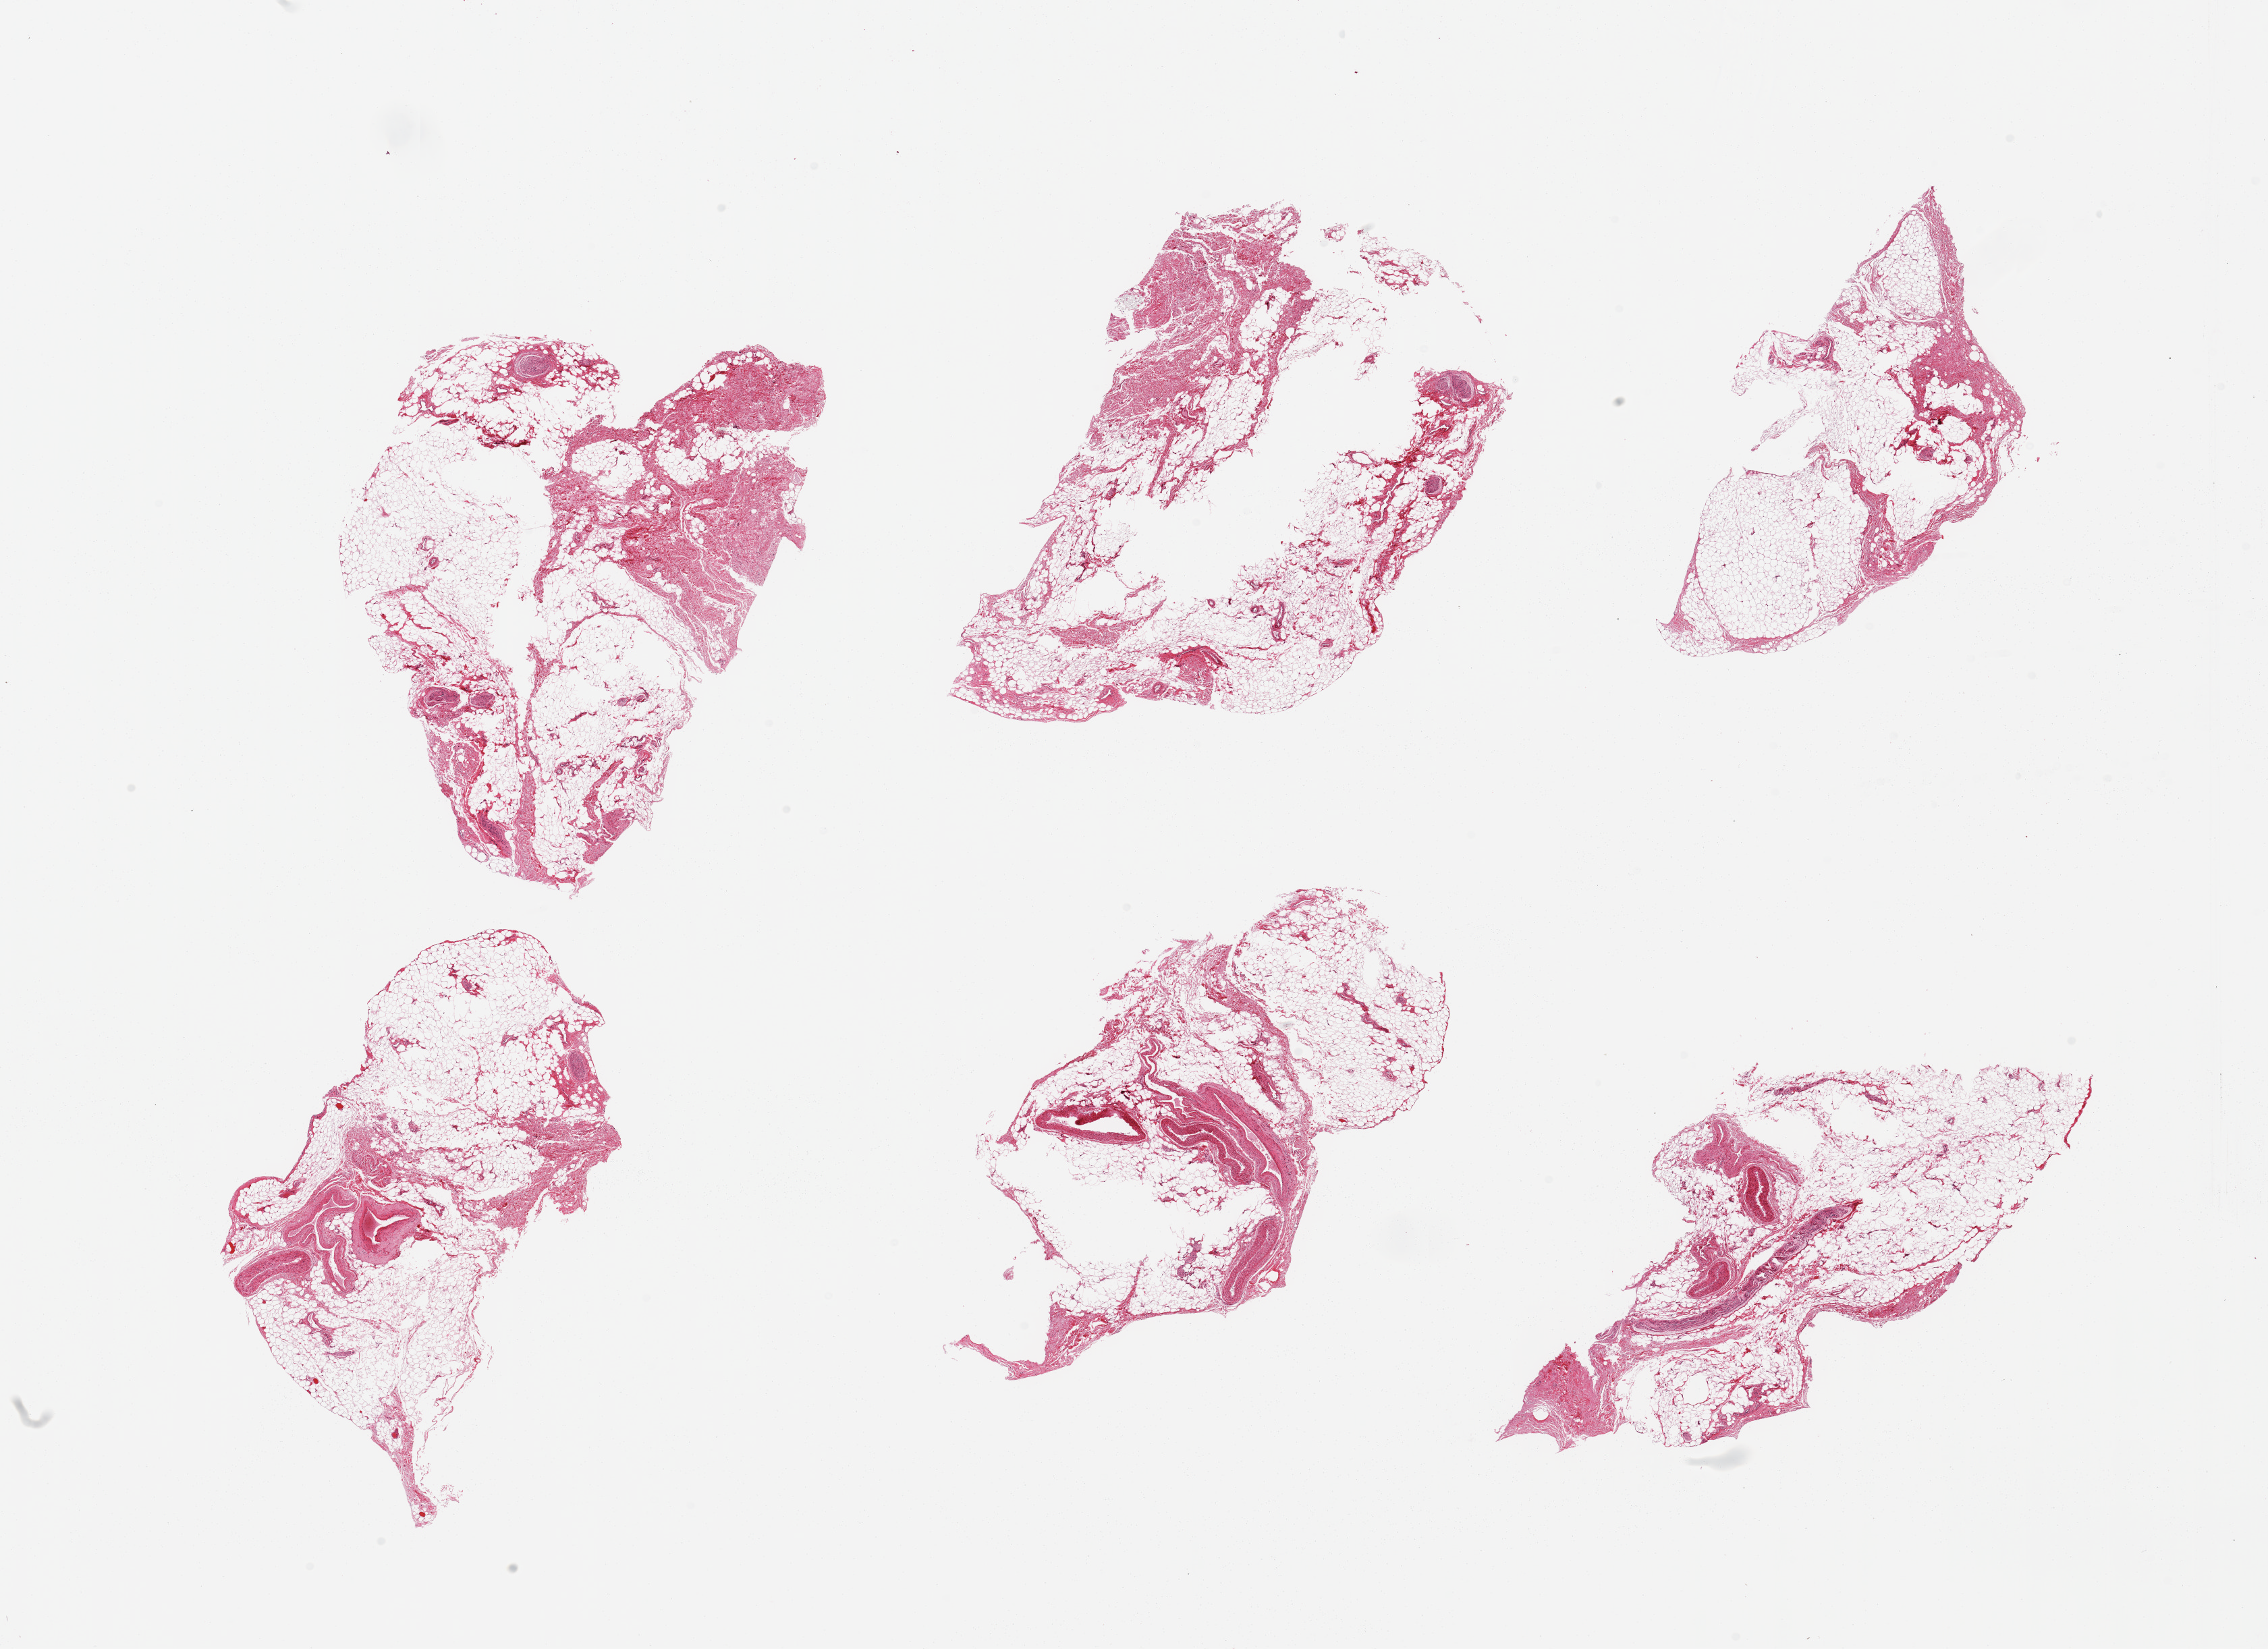
Whole-slide image, haematoxylin and eosin stain, brightfield, whole scanned area (about 26.6 x 19.3 mm) shown as a low-resolution overview; PAXgene-fixed paraffin-embedded (PFPE) section; target tissue: gastroesophageal junction; donor tissue sample.
Pathologist's review note for this sample: 6 pieces; fat/fibrous tissue/nerve/vessels, not muscularis.